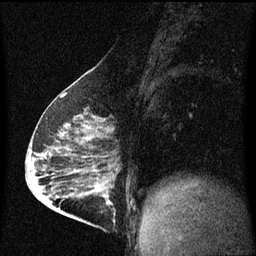
Breast MRI (dynamic contrast-enhanced), one sagittal slice. Dynamic contrast-enhanced series, image 2 of 3 at this slice position (ordered by acquisition). 1.5 T. TE 4.2 ms, TR 8 ms. 2 mm slice thickness. 256 × 256 image matrix, field of view 200 × 200 mm. Female patient, age 63 years.
Structures marked on this image (semi-automatic segmentation, software-assisted and operator-edited):
- analysis volume of interest (the breast-tissue region the enhancement analysis was run in; not a lesion): bounding box [x1, y1, x2, y2] px = [88, 182, 117, 229]
- tumour enhancement mask (voxels above the 70 % enhancement threshold inside the analysis volume of interest): [88, 190, 115, 215]